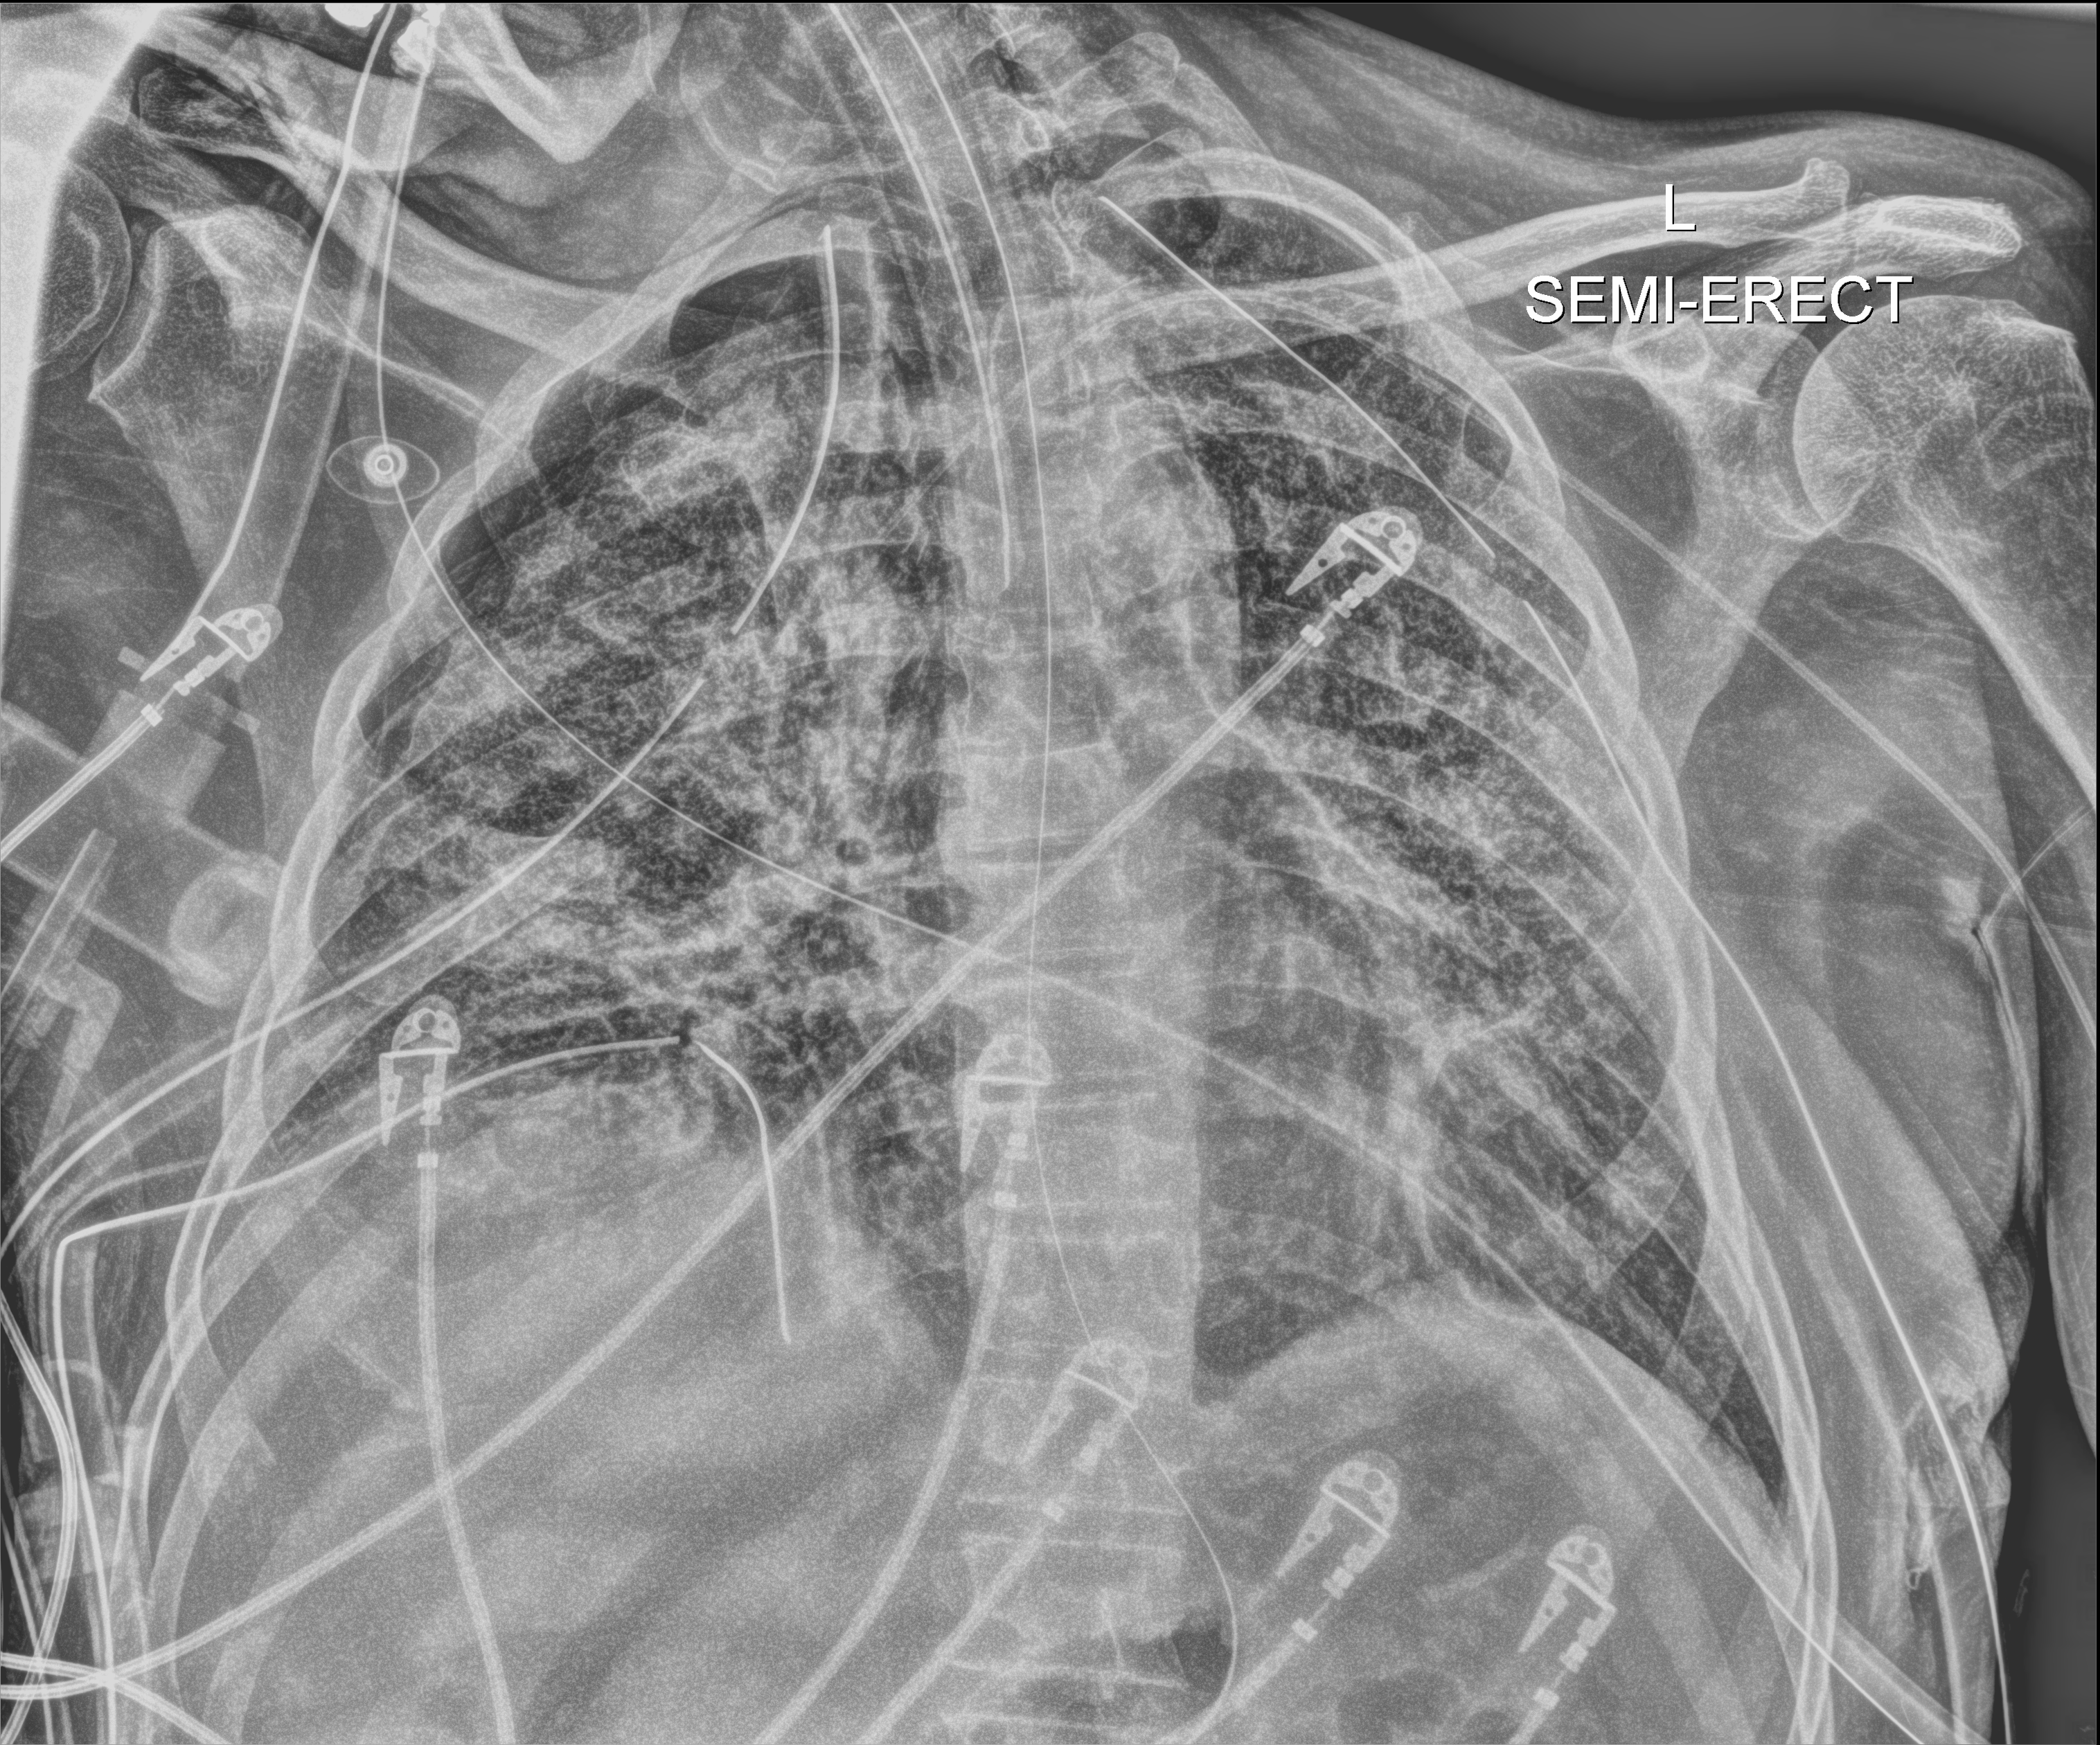
Chest X-ray (portable). Male patient hospitalised with COVID-19, age 18–59 years.
From the hospital-stay record, not from the radiograph (when in the stay this image was taken is not recorded): mechanically ventilated during this hospital stay: yes.